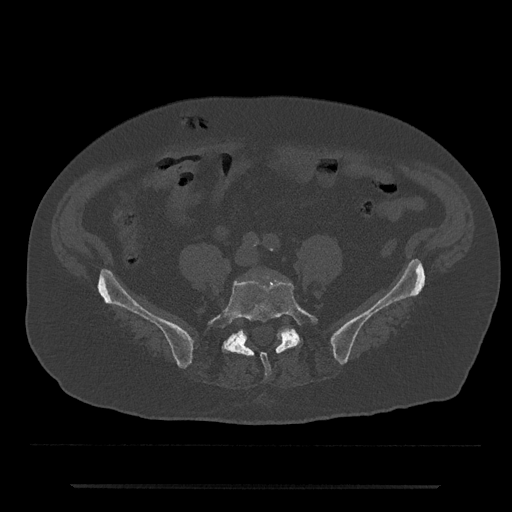
CT including the spine, one axial slice. Position 285 of 797 along the scan axis. Reconstruction kernel Br40s/3. Bone window (W 1800 / L 400 HU). 0.5 mm slice thickness. 512 × 512 image matrix, field of view 434 × 434 mm. Patient: male, 80 years. Case-level facts recorded for this patient, not image findings: primary cancer: prostate.
Annotated regions visible in this slice (semi-automatically segmented with operator editing):
- L5 vertebra: bounding box <208,280,318,377> (left, top, right, bottom; pixels)